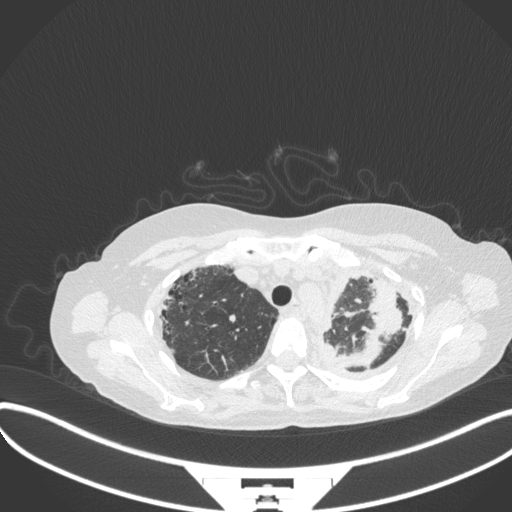
Chest CT, one axial slice. Position 277 of 373 along the scan axis. Reconstruction kernel B31f. 120 kVp. Lung window (W 1500 / L -600 HU). 1 mm slice thickness. 512 × 512 image matrix, field of view 400 × 400 mm. Female patient, age 56 years. From the clinical record (not read from this slice): clinical TNM (as recorded): T1 N0 M0.
Structures marked on this image (rectangle marked by the reading radiologist):
- lung tumour (recorded histology: adenocarcinoma): bounding box <337,274,402,368> (left, top, right, bottom; pixels)